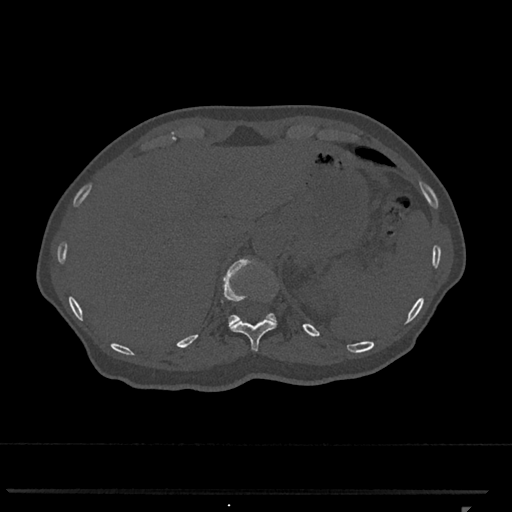
CT including the spine, one axial slice; slice 499 of 793 in the series (ordered by position); reconstruction kernel Br40s/3; bone window (W 1800 / L 400 HU); 0.5 mm slice thickness; 512 × 512 image matrix, field of view 380 × 380 mm. Female patient, age 62 years. From the clinical record (not read from this slice): primary cancer: renal.
Structures marked on this image (semi-automatic segmentation, software-assisted and operator-edited):
- T11 vertebra: bounding box <229,263,277,351> (left, top, right, bottom; pixels)
- T12 vertebra: <222,258,277,325>